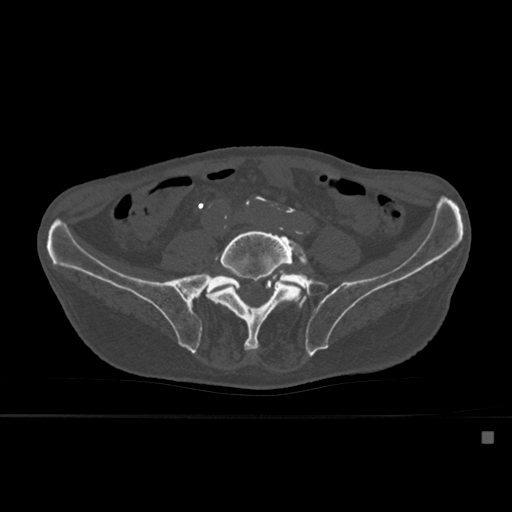
CT including the spine, one axial slice. Slice 174 of 527 in the series (ordered by position). Bone window (W 1800 / L 400 HU). 1.5 mm slice thickness. 512 × 512 image matrix, field of view 373 × 373 mm. Male patient, age 78 years. Case-level facts recorded for this patient, not image findings: primary cancer: prostate.
Structures marked on this image (semi-automatic segmentation, software-assisted and operator-edited):
- L4 vertebra: bounding box <279,299,288,303> (left, top, right, bottom; pixels)
- L5 vertebra: <207,230,308,350>